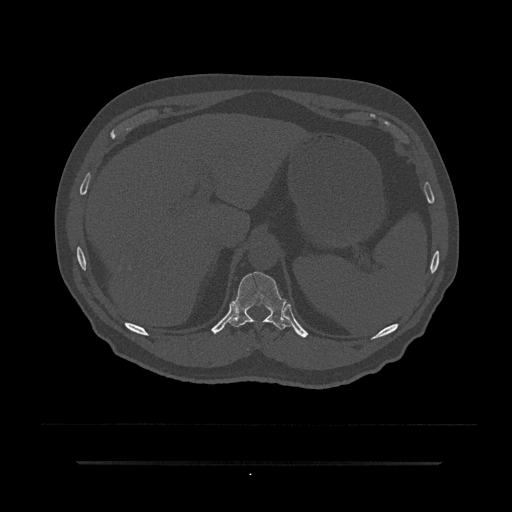
CT including the spine, one axial slice. Reconstruction kernel Br40s/3. 120 kVp. Bone window (W 1800 / L 400 HU). 512 × 512 image matrix. Patient: male, 59 years. Case-level facts recorded for this patient, not image findings: primary cancer: bile ducts.
Annotated regions visible in this slice (semi-automatically segmented with operator editing):
- T11 vertebra: bounding box [x1, y1, x2, y2] px = [229, 271, 295, 330]